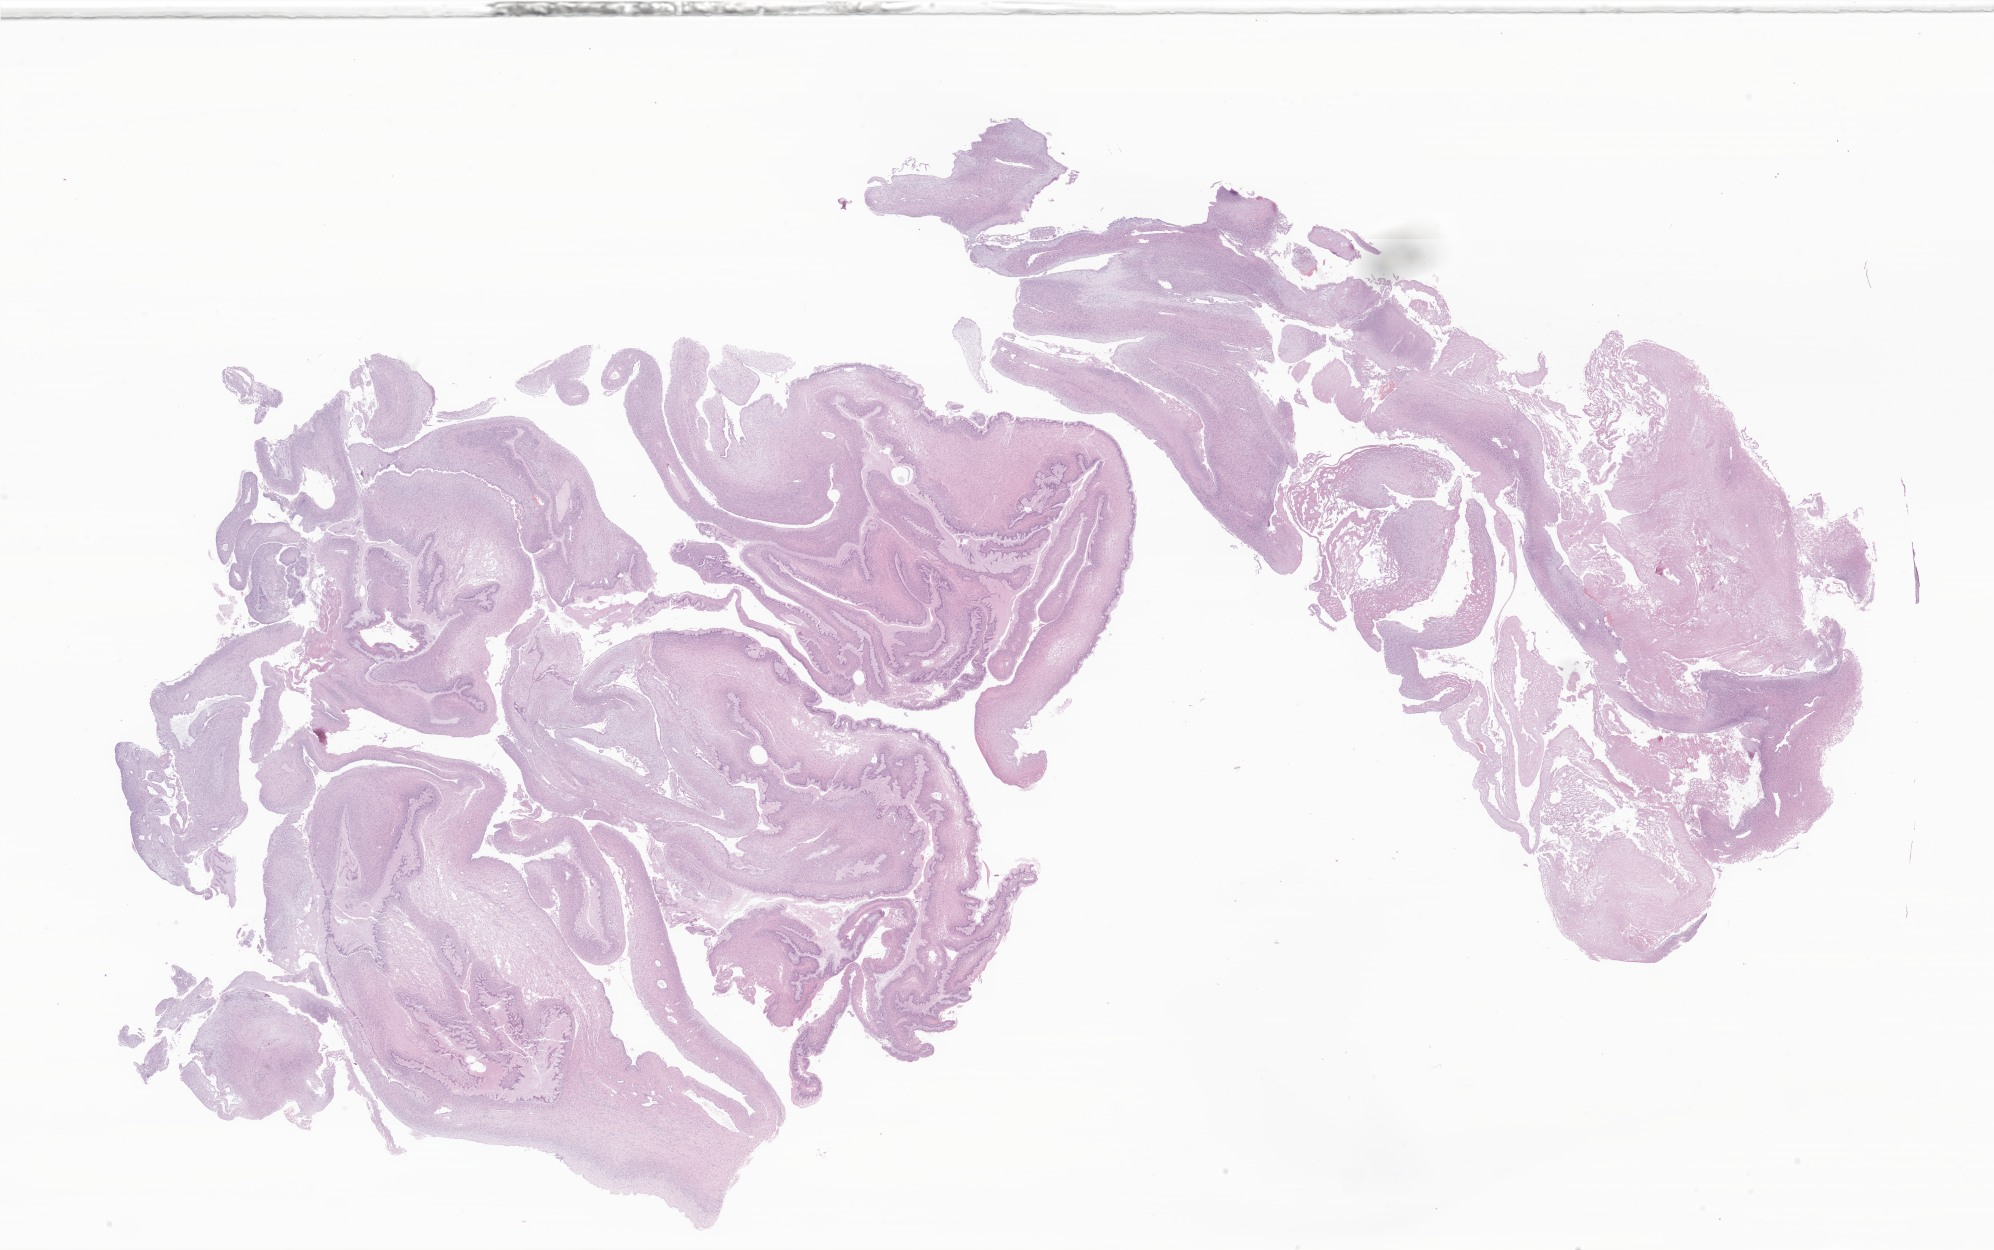
Whole-slide image, H&E stain of tumor tissue from the ovary — low-resolution overview of the scanned area, about 33.6 x 21.1 mm; FFPE section. Patient: female, age 312 months (26 years).
Diagnosis: Mucinous cystic tumor of borderline malignancy.